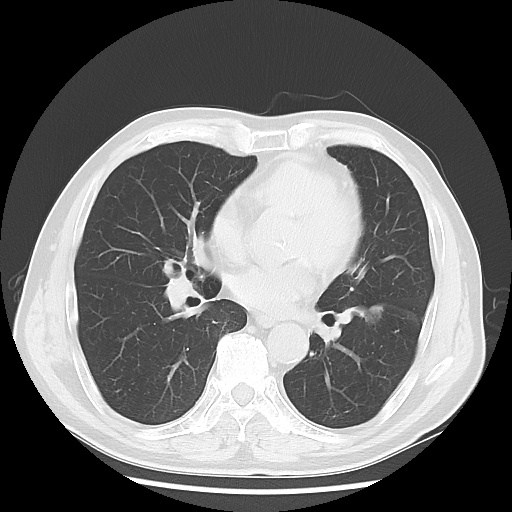
Chest CT, one axial slice. Slice 31 of 68 in the series (ordered by position). Reconstruction kernel LUNG. 120 kVp. Lung window (W 1500 / L -600 HU). 5 mm slice thickness. 512 × 512 image matrix. Male patient, age 71 years. From the clinical record (not read from this slice): clinical TNM (as recorded): T1c N1 M0.
Annotated regions visible in this slice (bounding box drawn by a radiologist):
- lung tumour (recorded histology: adenocarcinoma): bounding box <353,295,388,334> (left, top, right, bottom; pixels)